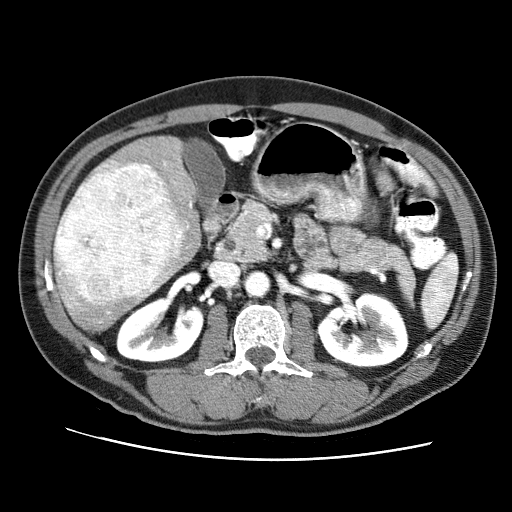
Contrast-enhanced abdominal CT (liver protocol), one axial slice; slice 34 of 71 in the series (ordered by position); reconstruction kernel STANDARD; 120 kVp; soft-tissue window (W 400 / L 40 HU); 2.5 mm slice thickness; 512 × 512 image matrix, field of view 360 × 360 mm. Case-level facts recorded for this patient, not image findings: diagnosis: hepatocellular carcinoma (patient treated with transarterial chemoembolisation; whether this scan precedes or follows treatment is not stated here); TNM stage (as recorded): Stage-II; Child-Pugh class: A; tumour differentiation: well differentiated; tumour nodularity: multinodular.
Structures marked on this image (semi-automatic segmentation, software-assisted and operator-edited):
- liver parenchyma outside the tumour (the mass and vessels are separate outlines, so this box may not span the whole liver): box from (x=56, y=135) to (x=201, y=330) px
- mass: (x=54, y=159)–(x=182, y=310)
- liver vessels: (x=107, y=163)–(x=192, y=313)